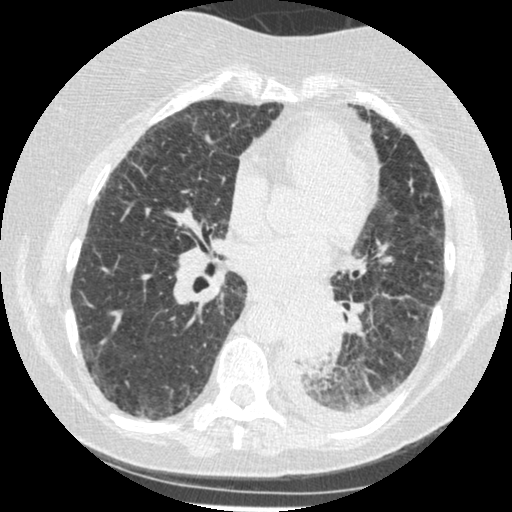
Chest CT (low-dose screening protocol), one axial image; third screening round (two years after baseline); lung window (W 1500 / L -600 HU); 1.25 mm slice thickness. Female participant, aged 60 years at enrolment.
Expert reader's lesion annotation, bounding box [x1, y1, x2, y2] px = [275, 304, 343, 376]. The exam's reader record, not a measurement of the box and not confirmed to be the same lesion: non-calcified nodule or mass ≥4 mm, left lower lobe, 54 × 38 mm, smooth margins, soft tissue attenuation, pre-existing on the prior screen: yes; interval growth: yes. Later outcome: lung cancer diagnosed 15 days after this screen — small cell carcinoma, NOS, left lower lobe, undifferentiated (G4), stage IV (AJCC 6th edition), 69 mm at pathology.